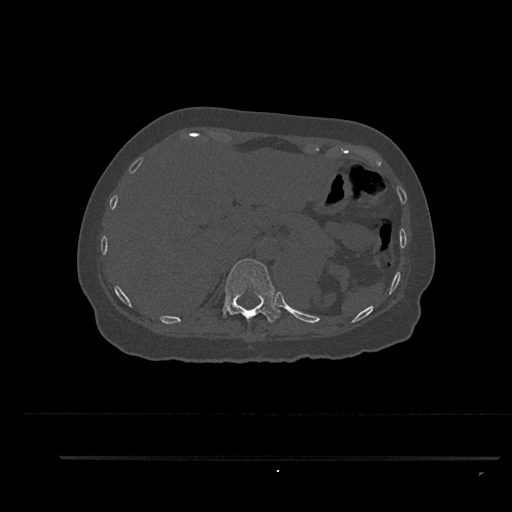
CT including the spine, one axial slice; slice 318 of 797 in the series (ordered by position); 120 kVp; bone window (W 1800 / L 400 HU); 0.5 mm slice thickness; 512 × 512 image matrix. Female patient, age 44 years. Case-level facts recorded for this patient, not image findings: primary cancer: renal; vertebrae with lytic lesions (as recorded): L1.
Annotated regions visible in this slice (semi-automatically segmented with operator editing):
- T11 vertebra: bounding box [x1, y1, x2, y2] px = [223, 259, 280, 322]